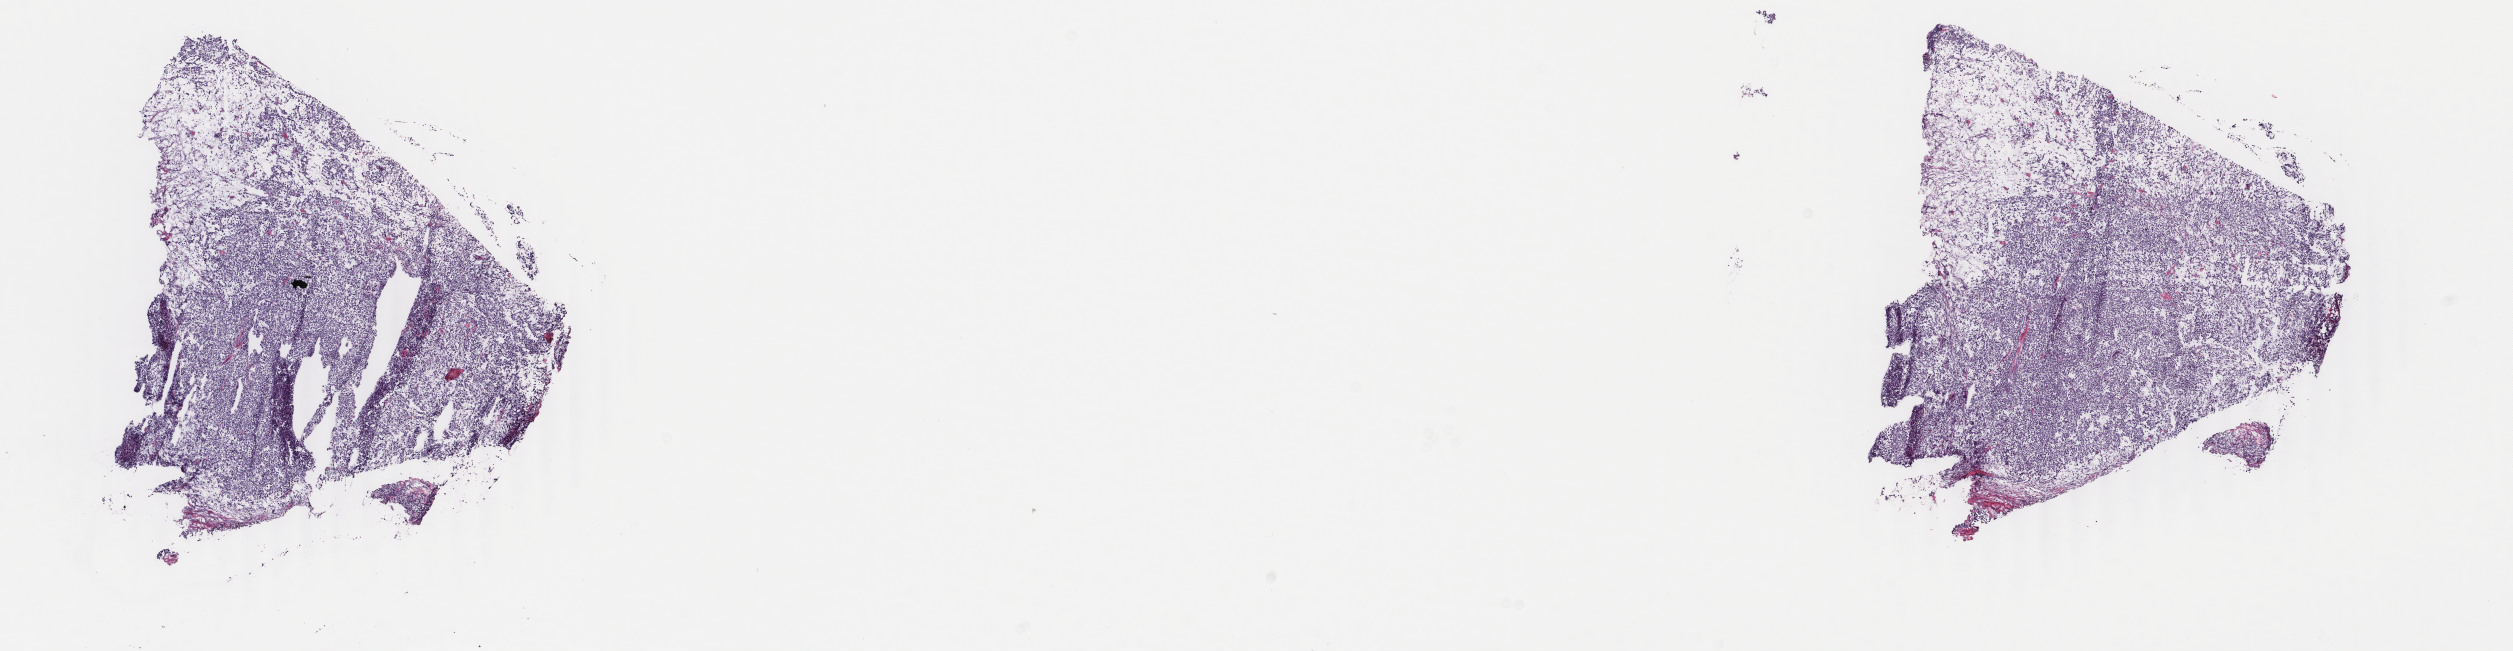
Whole-slide histology image, Hematoxylin and eosin (H&E) stained — a low-resolution overview of the entire scanned area, about 20.0 x 5.2 mm; frozen section; metastatic tumour sample, sampled site: connective, subcutaneous and other soft tissues of trunk. Male, age 46 years at initial diagnosis. Pathologist review of this section (percent, as recorded): tumour cells 100%, tumour nuclei 95%, normal cells 0%, stromal cells 0%, necrosis 0%. Inflammatory infiltration, as recorded: lymphocyte infiltration 0%, monocyte infiltration 0%, neutrophil infiltration 0%.
This section: metastatic tumour tissue. Patient diagnosis: Malignant melanoma, NOS.